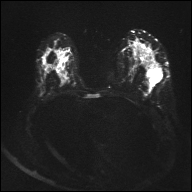
Breast MRI, one axial slice. Position 20 of 32 along the scan axis. Diffusion-weighted series; image 2 of 4 stored at this slice position (different b-values; order by instance number). 1.5 T. 4 mm slice thickness. 192 × 192 image matrix, field of view 360 × 360 mm. Female patient.
Annotated regions visible in this slice (manually delineated by an expert):
- tumour on diffusion-weighted imaging: bounding box [x1, y1, x2, y2] px = [148, 69, 161, 80]